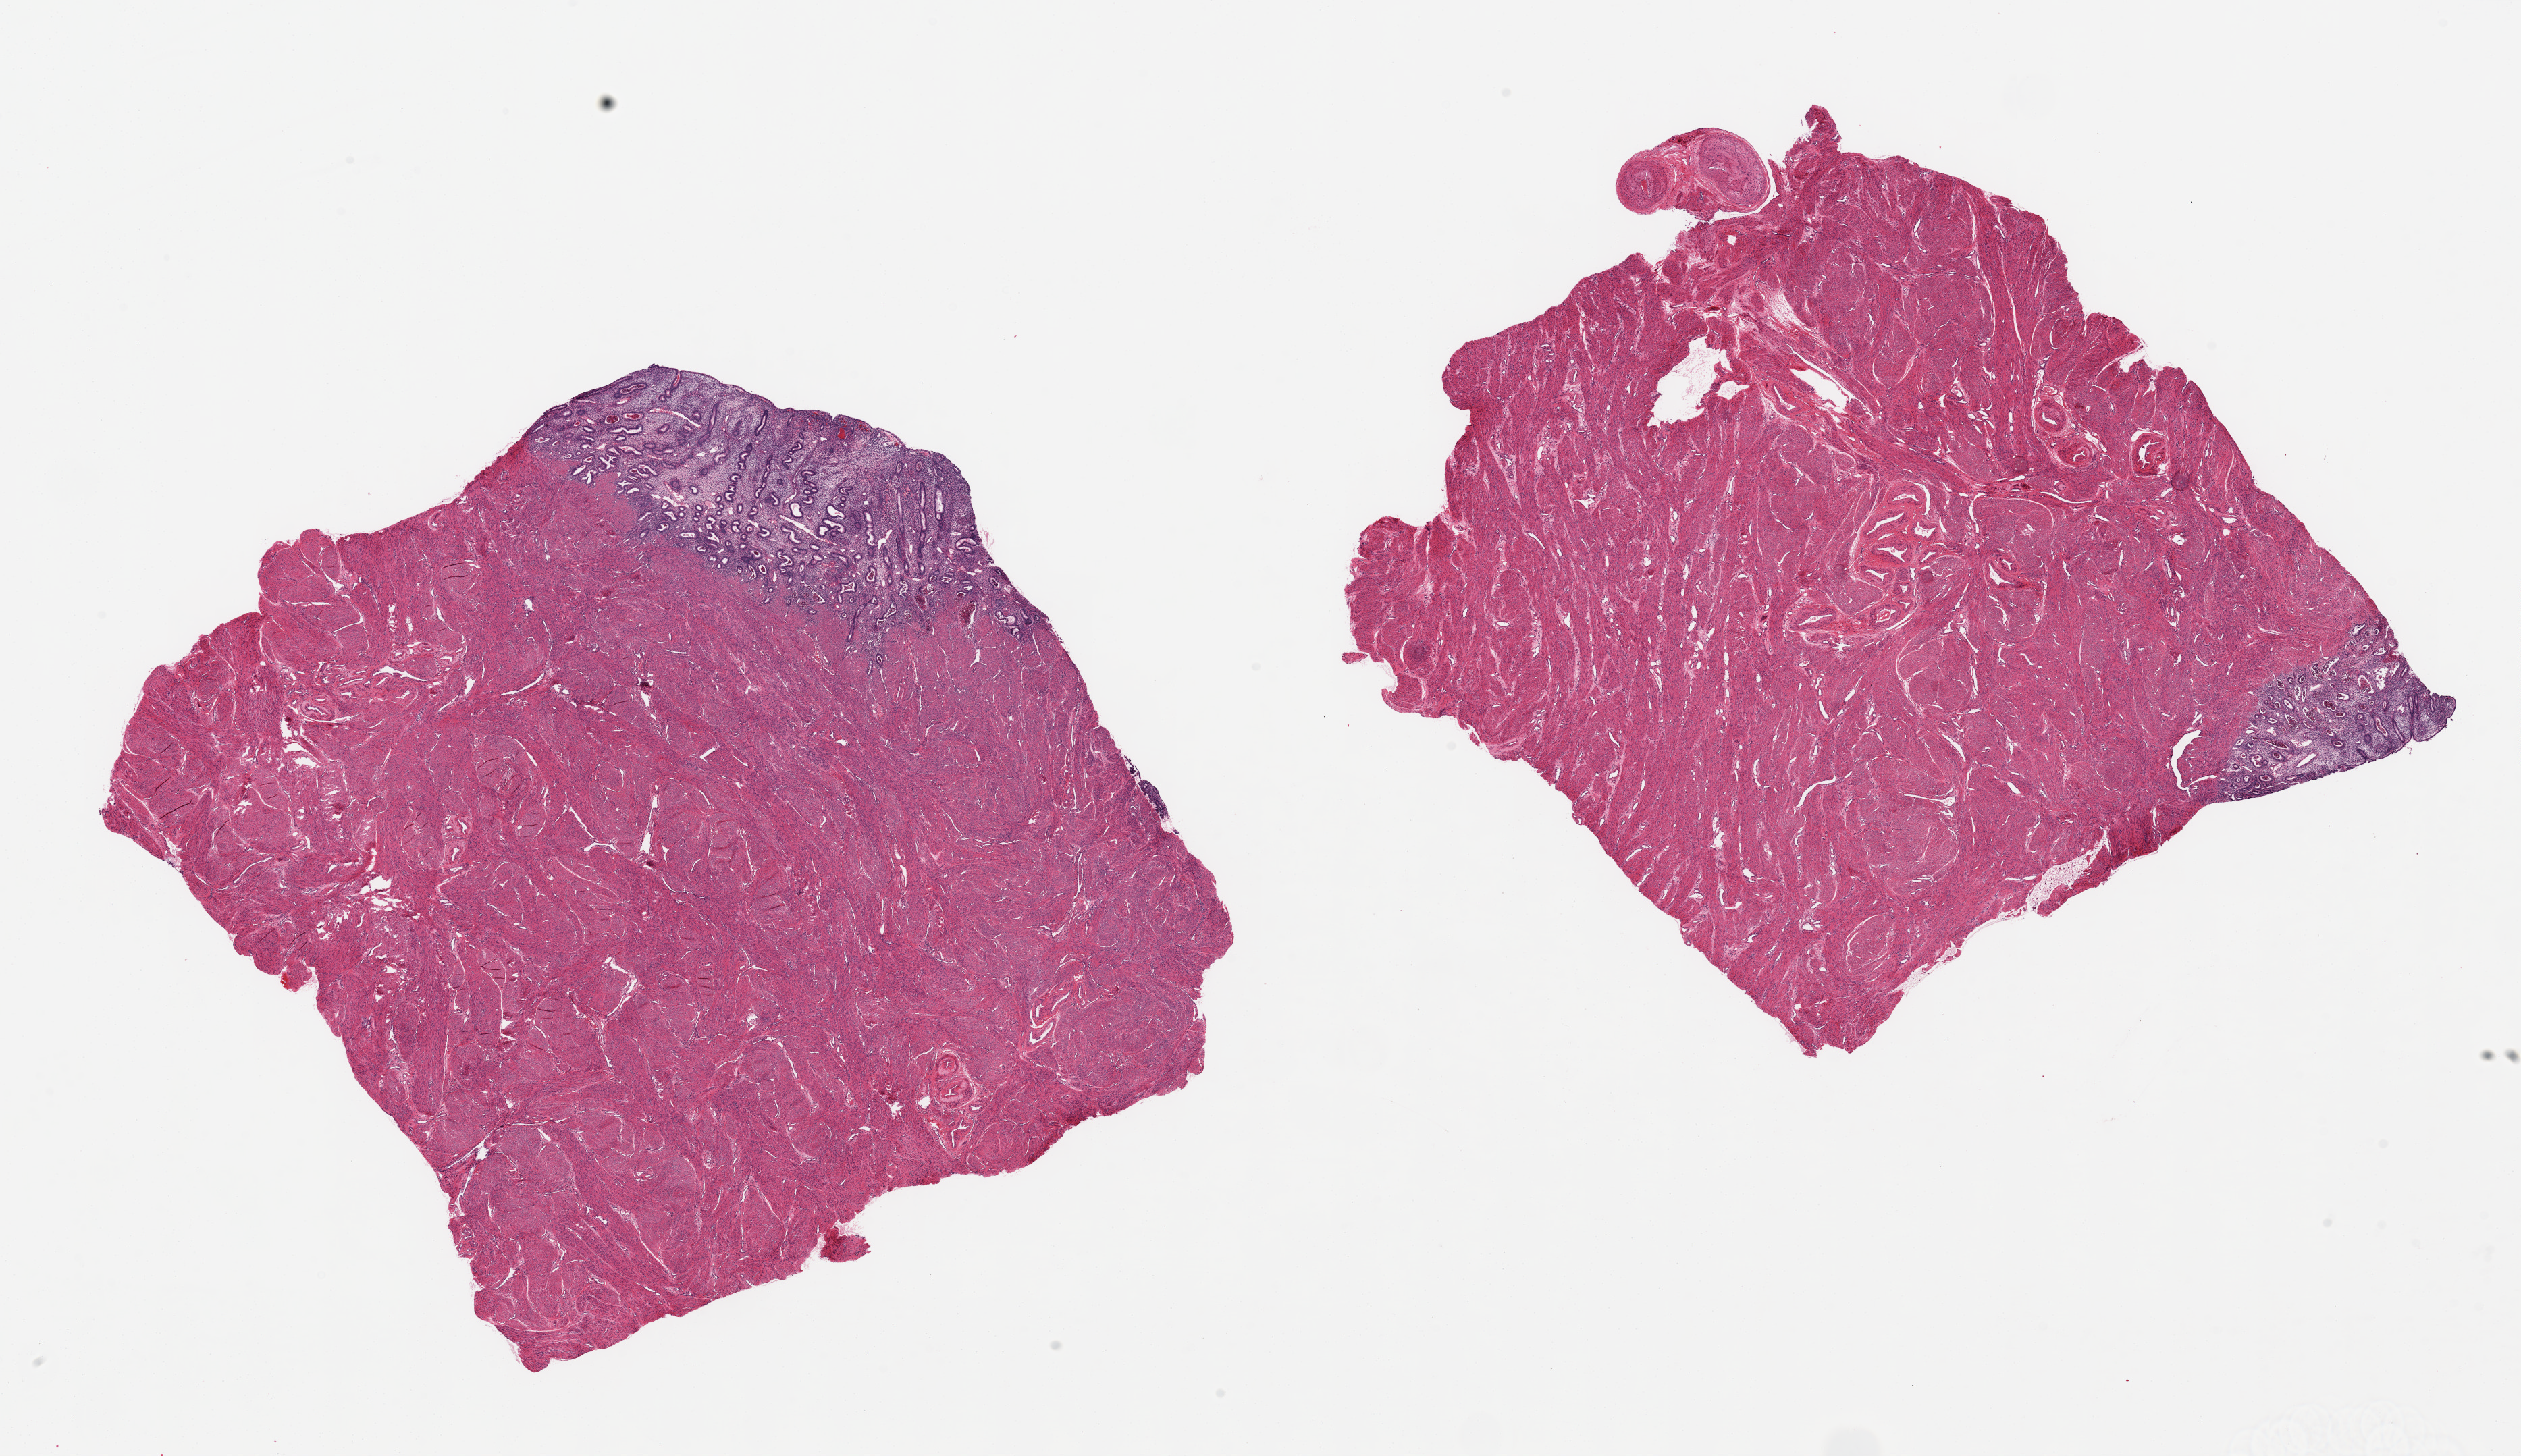
Digitized H&E-stained section — shown as a low-resolution overview of the whole scanned area (about 29.5 x 17.1 mm, from a 20x scan). PAXgene-fixed paraffin-embedded (PFPE) section. Target tissue: uterus. Tissue donor sample. Donor sex: female.
Reviewer comment on this tissue sample: 2 aliquots, ~9x9mm. Well preserved 7x2mm (aggregate) proliferative phase pattern endometrium.